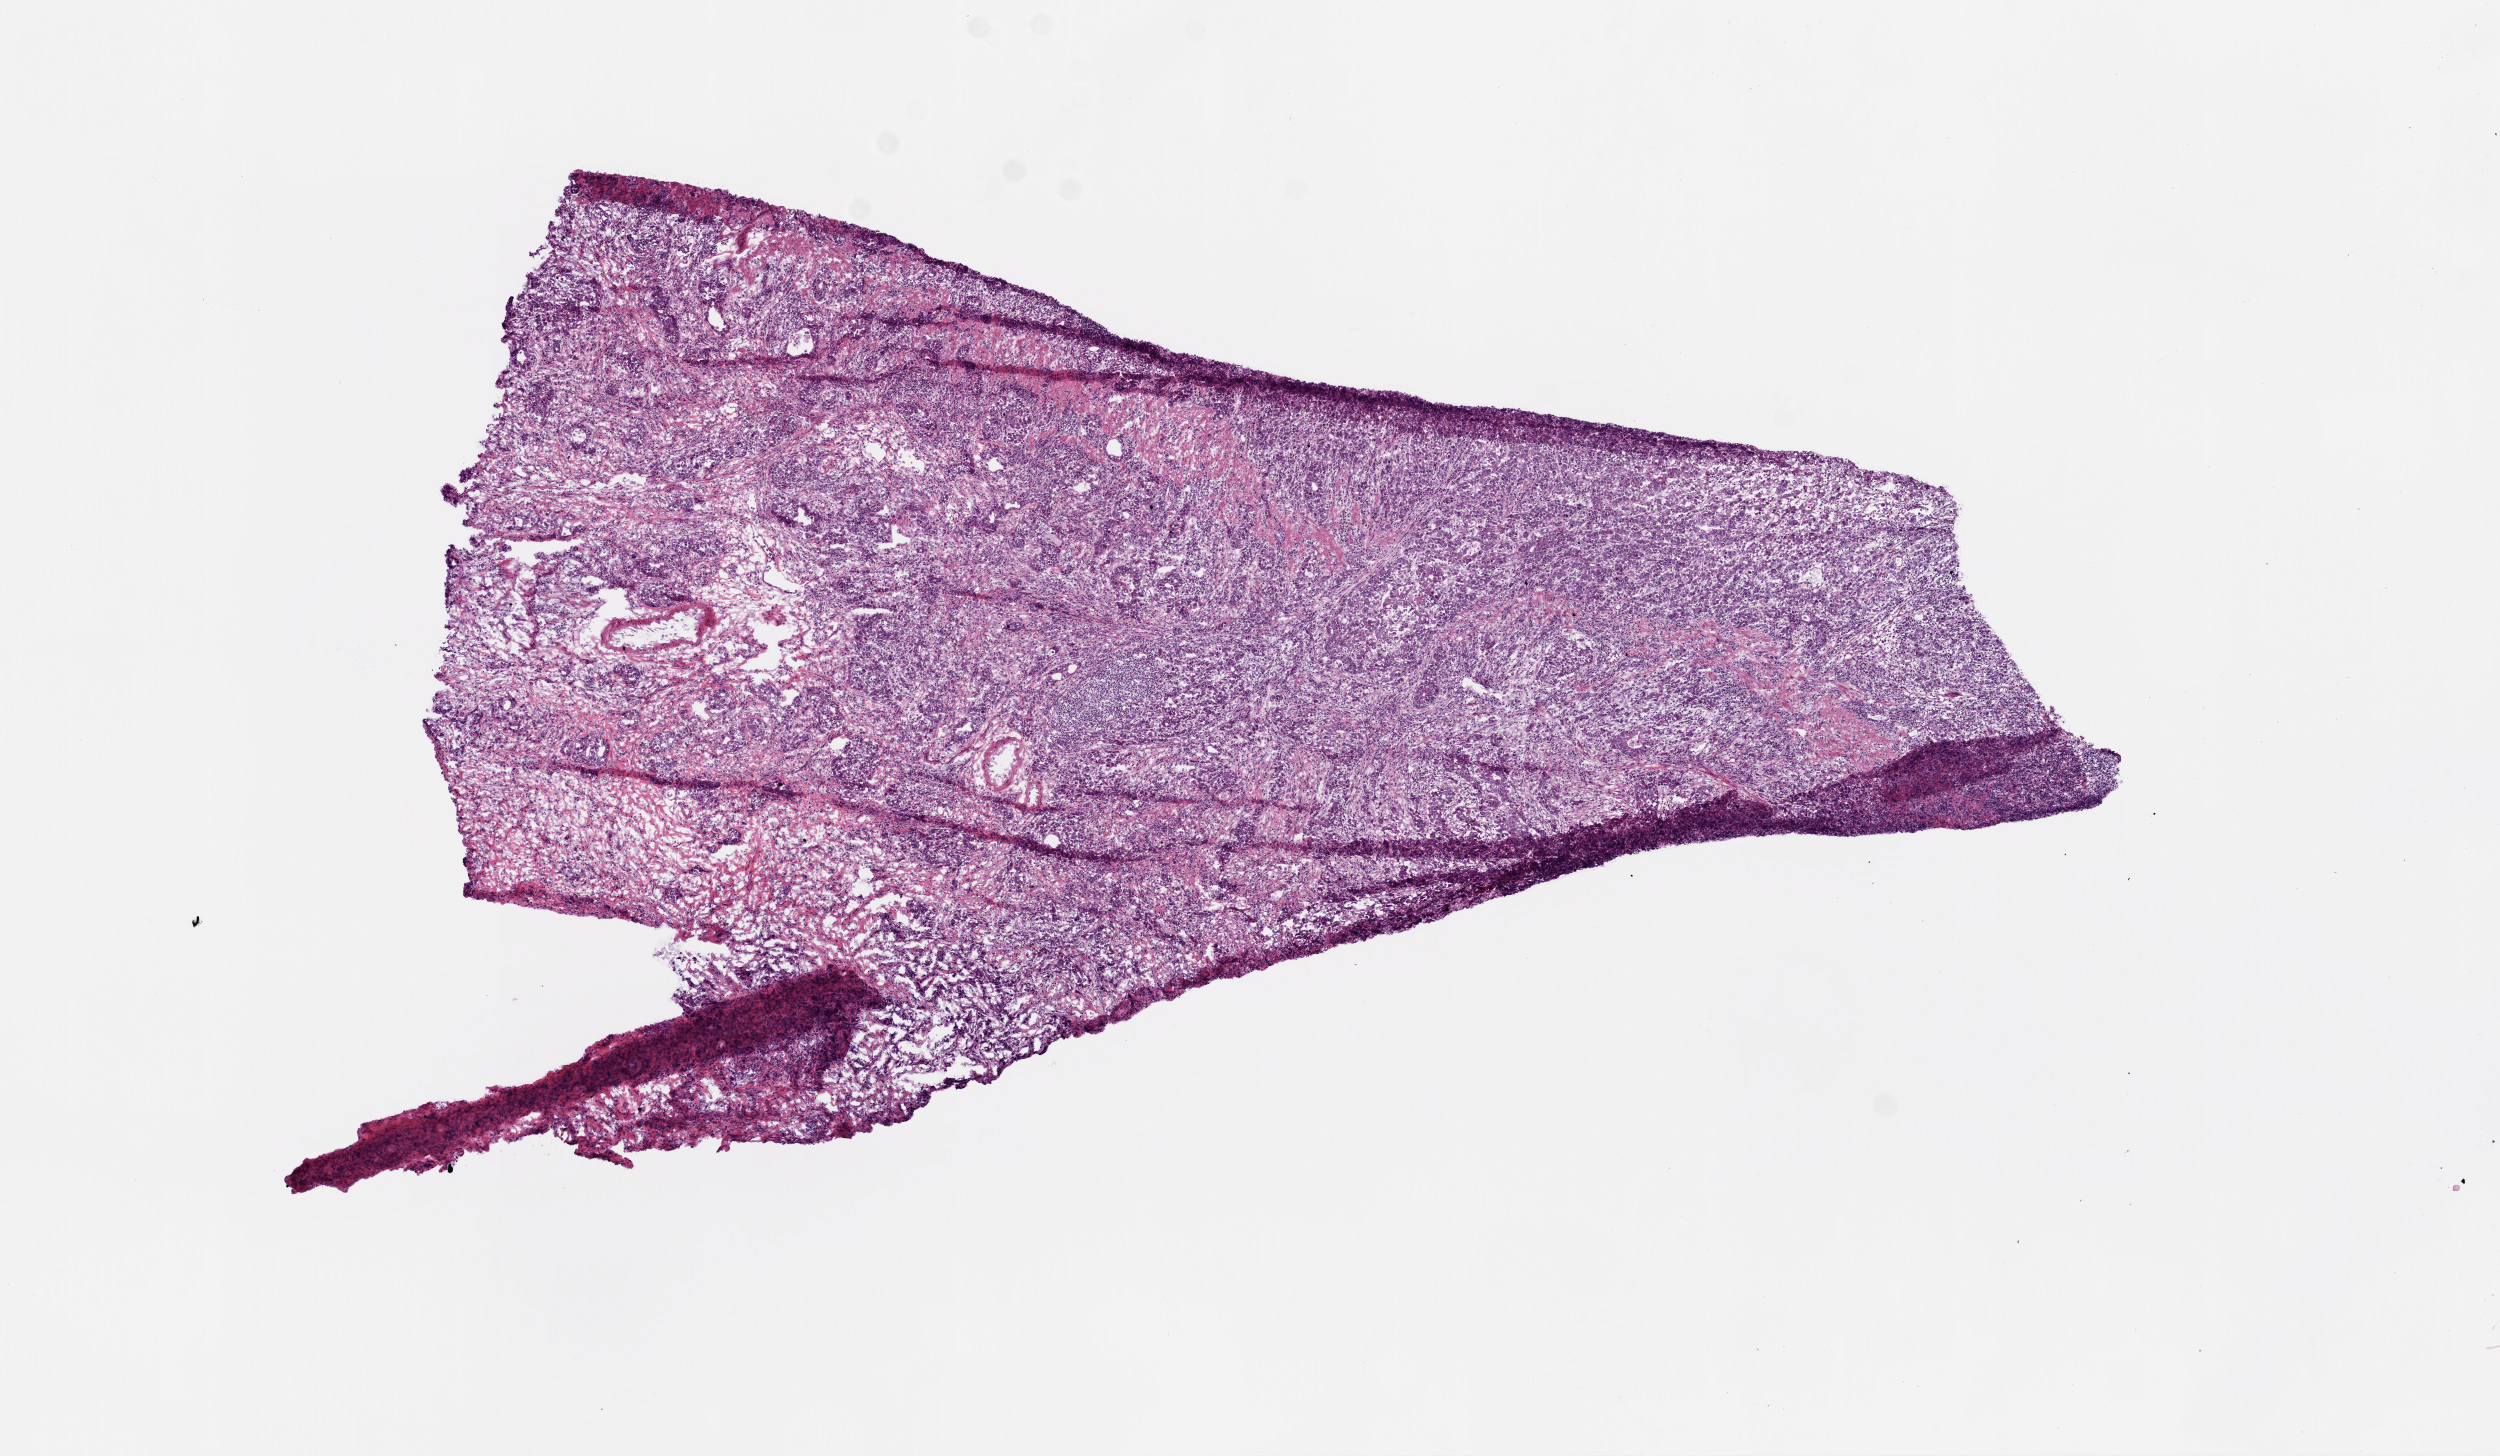
Digitized H&E tissue section (whole slide) — a low-resolution overview of the entire scanned area, about 10.0 x 5.8 mm (from a 20x scan); frozen section from the bottom of the tissue portion; stomach, primary tumour sample. Male patient; age at initial diagnosis 68 years. Histologic grade: G3 (poorly differentiated). Pathologist review of this section (percent, as recorded): tumour cells 85%, tumour nuclei 75%, normal cells 0%, stromal cells 15%, necrosis 0%.
• histologic diagnosis: Adenocarcinoma, intestinal type (body of stomach)
• AJCC pathologic stage: IIIA (5th edition)